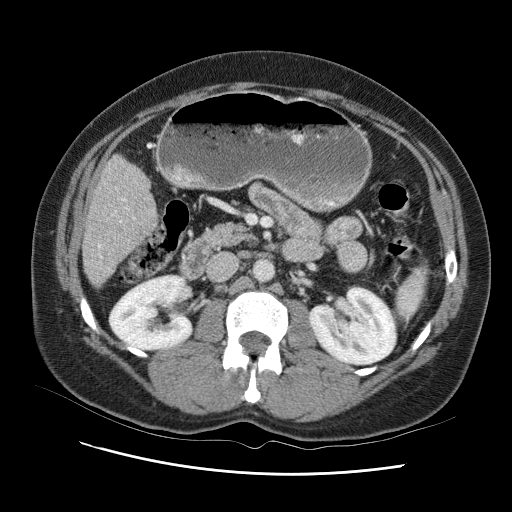
Contrast-enhanced abdominal CT (liver protocol), one axial slice; position 32 of 95 along the scan axis; reconstruction kernel STANDARD; one of 2 acquisitions stored at this slice position; soft-tissue window (W 400 / L 40 HU); 2.5 mm slice thickness; 512 × 512 image matrix, field of view 360 × 360 mm. From the clinical record (not read from this slice): diagnosis: hepatocellular carcinoma (patient treated with transarterial chemoembolisation; whether this scan precedes or follows treatment is not stated here); TNM stage (as recorded): Stage-I; Child-Pugh class: B; tumour differentiation: moderately differentiated; tumour nodularity: uninodular.
Outlined on this slice (semi-automatic segmentation, software-assisted and operator-edited):
- liver parenchyma outside the tumour (the mass and vessels are separate outlines, so this box may not span the whole liver): bounding box (x1, y1, x2, y2) in pixels: (82, 142, 164, 295)
- liver vessels: (99, 174, 147, 250)